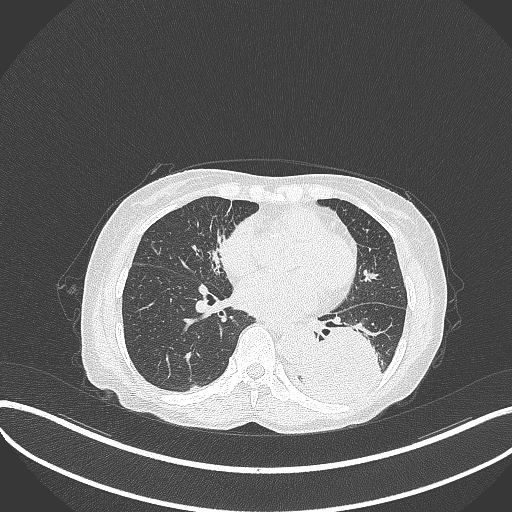
Chest CT, one axial slice; position 133 of 370 along the scan axis; reconstruction kernel B70f; lung window (W 1500 / L -600 HU); 512 × 512 image matrix, field of view 400 × 400 mm. Female patient, age 78 years. Case-level facts recorded for this patient, not image findings: clinical TNM (as recorded): T3 N0 M1.
Annotated regions visible in this slice (rectangle marked by the reading radiologist):
- lung tumour (recorded histology: squamous cell carcinoma): bounding box [x1, y1, x2, y2] px = [293, 323, 386, 411]